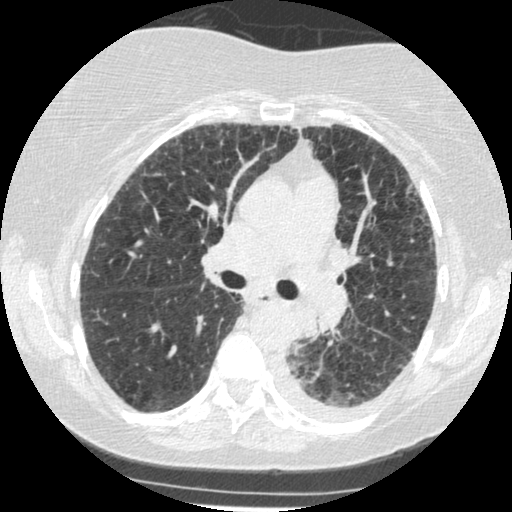
Low-dose screening chest CT, one axial slice; position 161 of 341 along the scan axis; reconstruction kernel STANDARD; lung window (W 1500 / L -600 HU); 1.25 mm slice thickness; 512 × 512 image matrix, field of view 310 × 310 mm.
Annotated regions visible in this slice (outlined manually by an expert reader):
- lesion 1 (tumor, lower lobe of left lung): bounding box <293,306,318,338> (left, top, right, bottom; pixels)